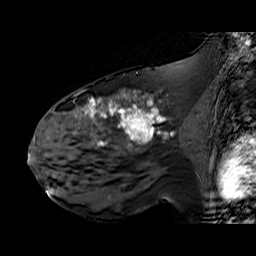
Breast MRI (dynamic contrast-enhanced), one sagittal slice; slice 33 of 60 in the series (ordered by position); dynamic contrast-enhanced series, time point 2 of 6 at this slice position (early post-contrast); 1.5 T; TE 6.3 ms, TR 32.9 ms; 4 mm slice thickness; 256 × 256 image matrix. Female patient. Case-level facts recorded for this patient, not image findings: setting: breast cancer imaged before/during neoadjuvant chemotherapy; receptor status: HER2-positive.
Outlined on this slice (semi-automatically segmented with operator editing):
- analysis volume of interest (the breast-tissue region the enhancement analysis was run in; not a lesion): box from (x=48, y=92) to (x=195, y=174) px
- tumour enhancement mask (voxels above the 100 % enhancement threshold inside the analysis volume of interest): (x=75, y=92)–(x=165, y=146)